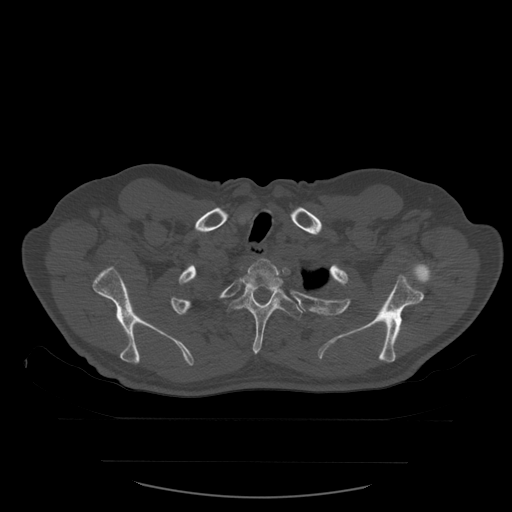
CT including the spine, one axial slice. Position 464 of 590 along the scan axis. Bone window (W 1800 / L 400 HU). 1.25 mm slice thickness. 512 × 512 image matrix, field of view 479 × 479 mm. Patient age 71 years. From the clinical record (not read from this slice): primary cancer: lung; vertebrae with lytic lesions (as recorded): T1, T2, L5, S1.
Structures marked on this image (semi-automatically segmented with operator editing):
- T2 vertebra: box from (x=243, y=258) to (x=284, y=290) px
- T3 vertebra: (x=225, y=289)–(x=303, y=355)